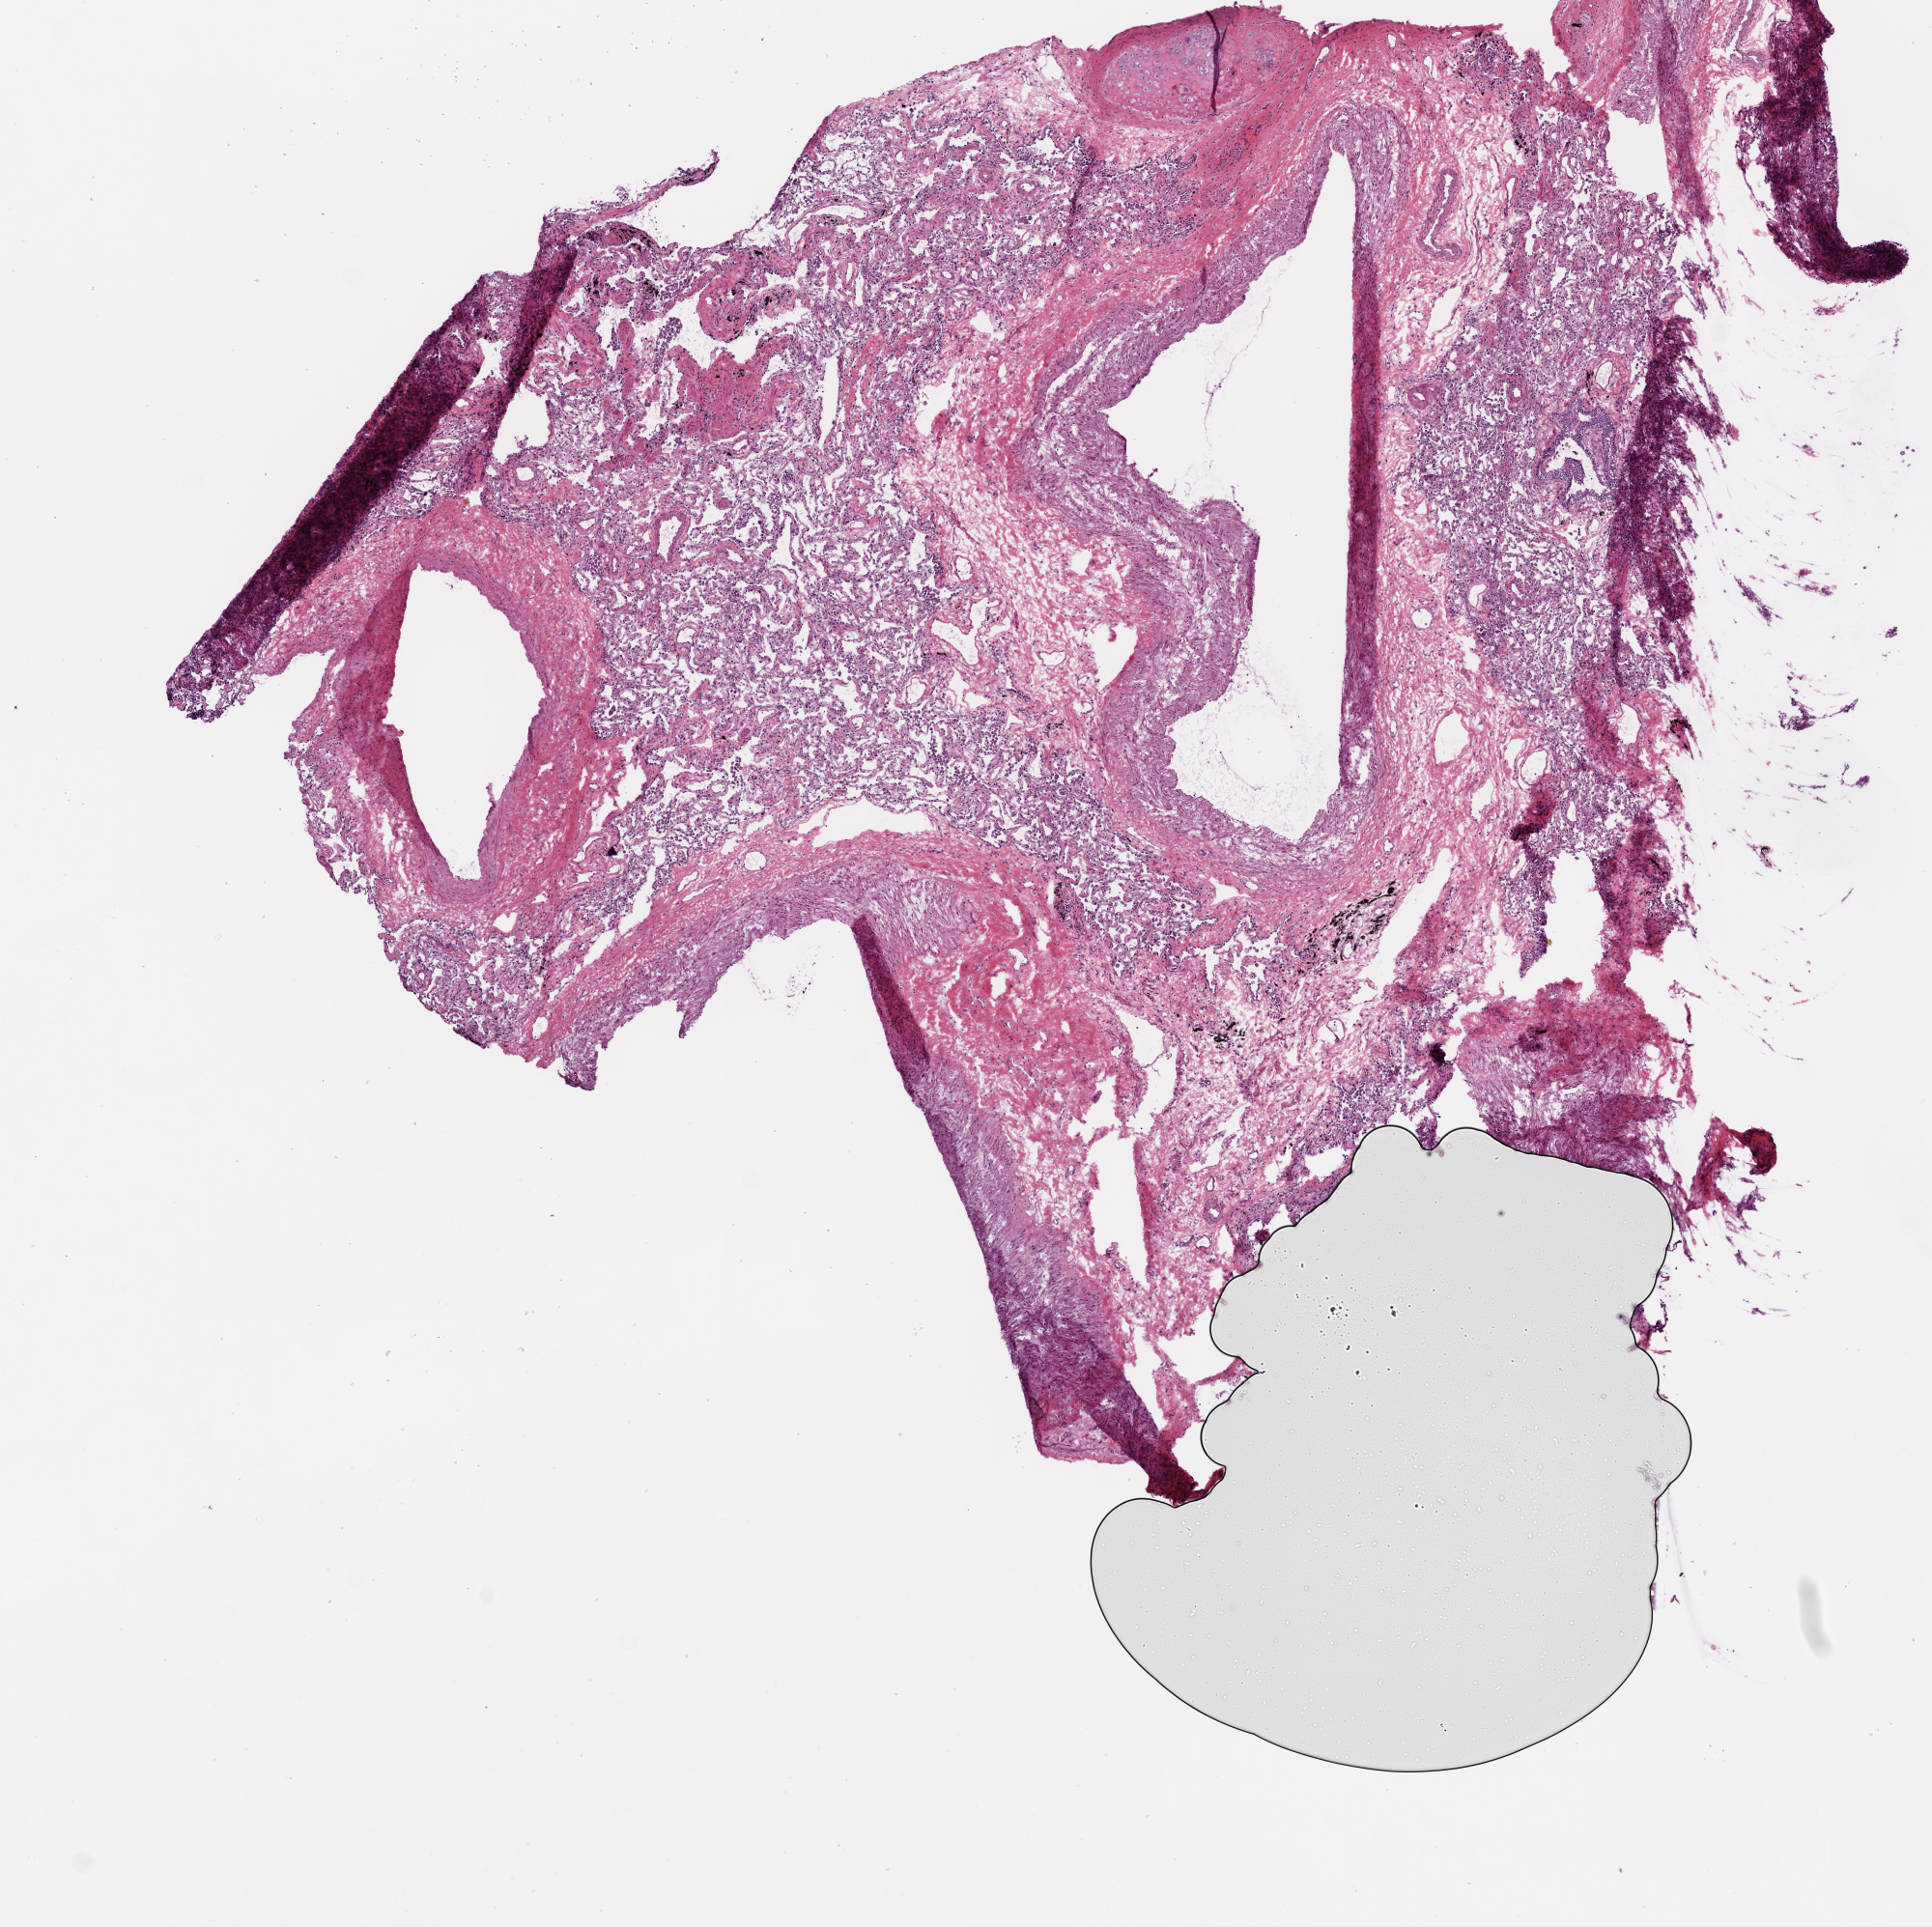
H&E-stained whole-slide image, whole scanned area (about 8.0 x 8.0 mm, slide scanned at 20x) shown as a low-resolution overview; frozen section from the top of the tissue portion; solid tissue normal (non-tumour tissue) sample from the lung. Female patient; age at initial diagnosis 72 years.
This section: solid tissue normal sample (biorepository sample class). Patient diagnosis: Adenocarcinoma, NOS.